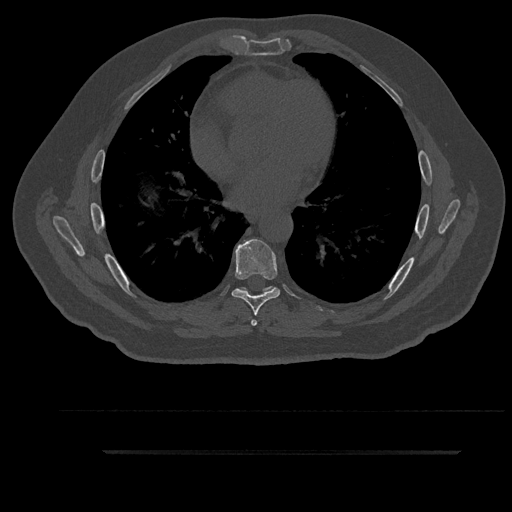
CT including the spine, one axial slice; position 520 of 797 along the scan axis; reconstruction kernel Br40s/3; 120 kVp; bone window (W 1800 / L 400 HU); 0.5 mm slice thickness; 512 × 512 image matrix, field of view 432 × 432 mm. Male patient, age 63 years. Case-level facts recorded for this patient, not image findings: primary cancer: renal.
Annotated regions visible in this slice (semi-automatic segmentation, software-assisted and operator-edited):
- T6 vertebra: bounding box <239,287,274,326> (left, top, right, bottom; pixels)
- T7 vertebra: <231,239,280,316>
- T8 vertebra: <242,285,273,291>